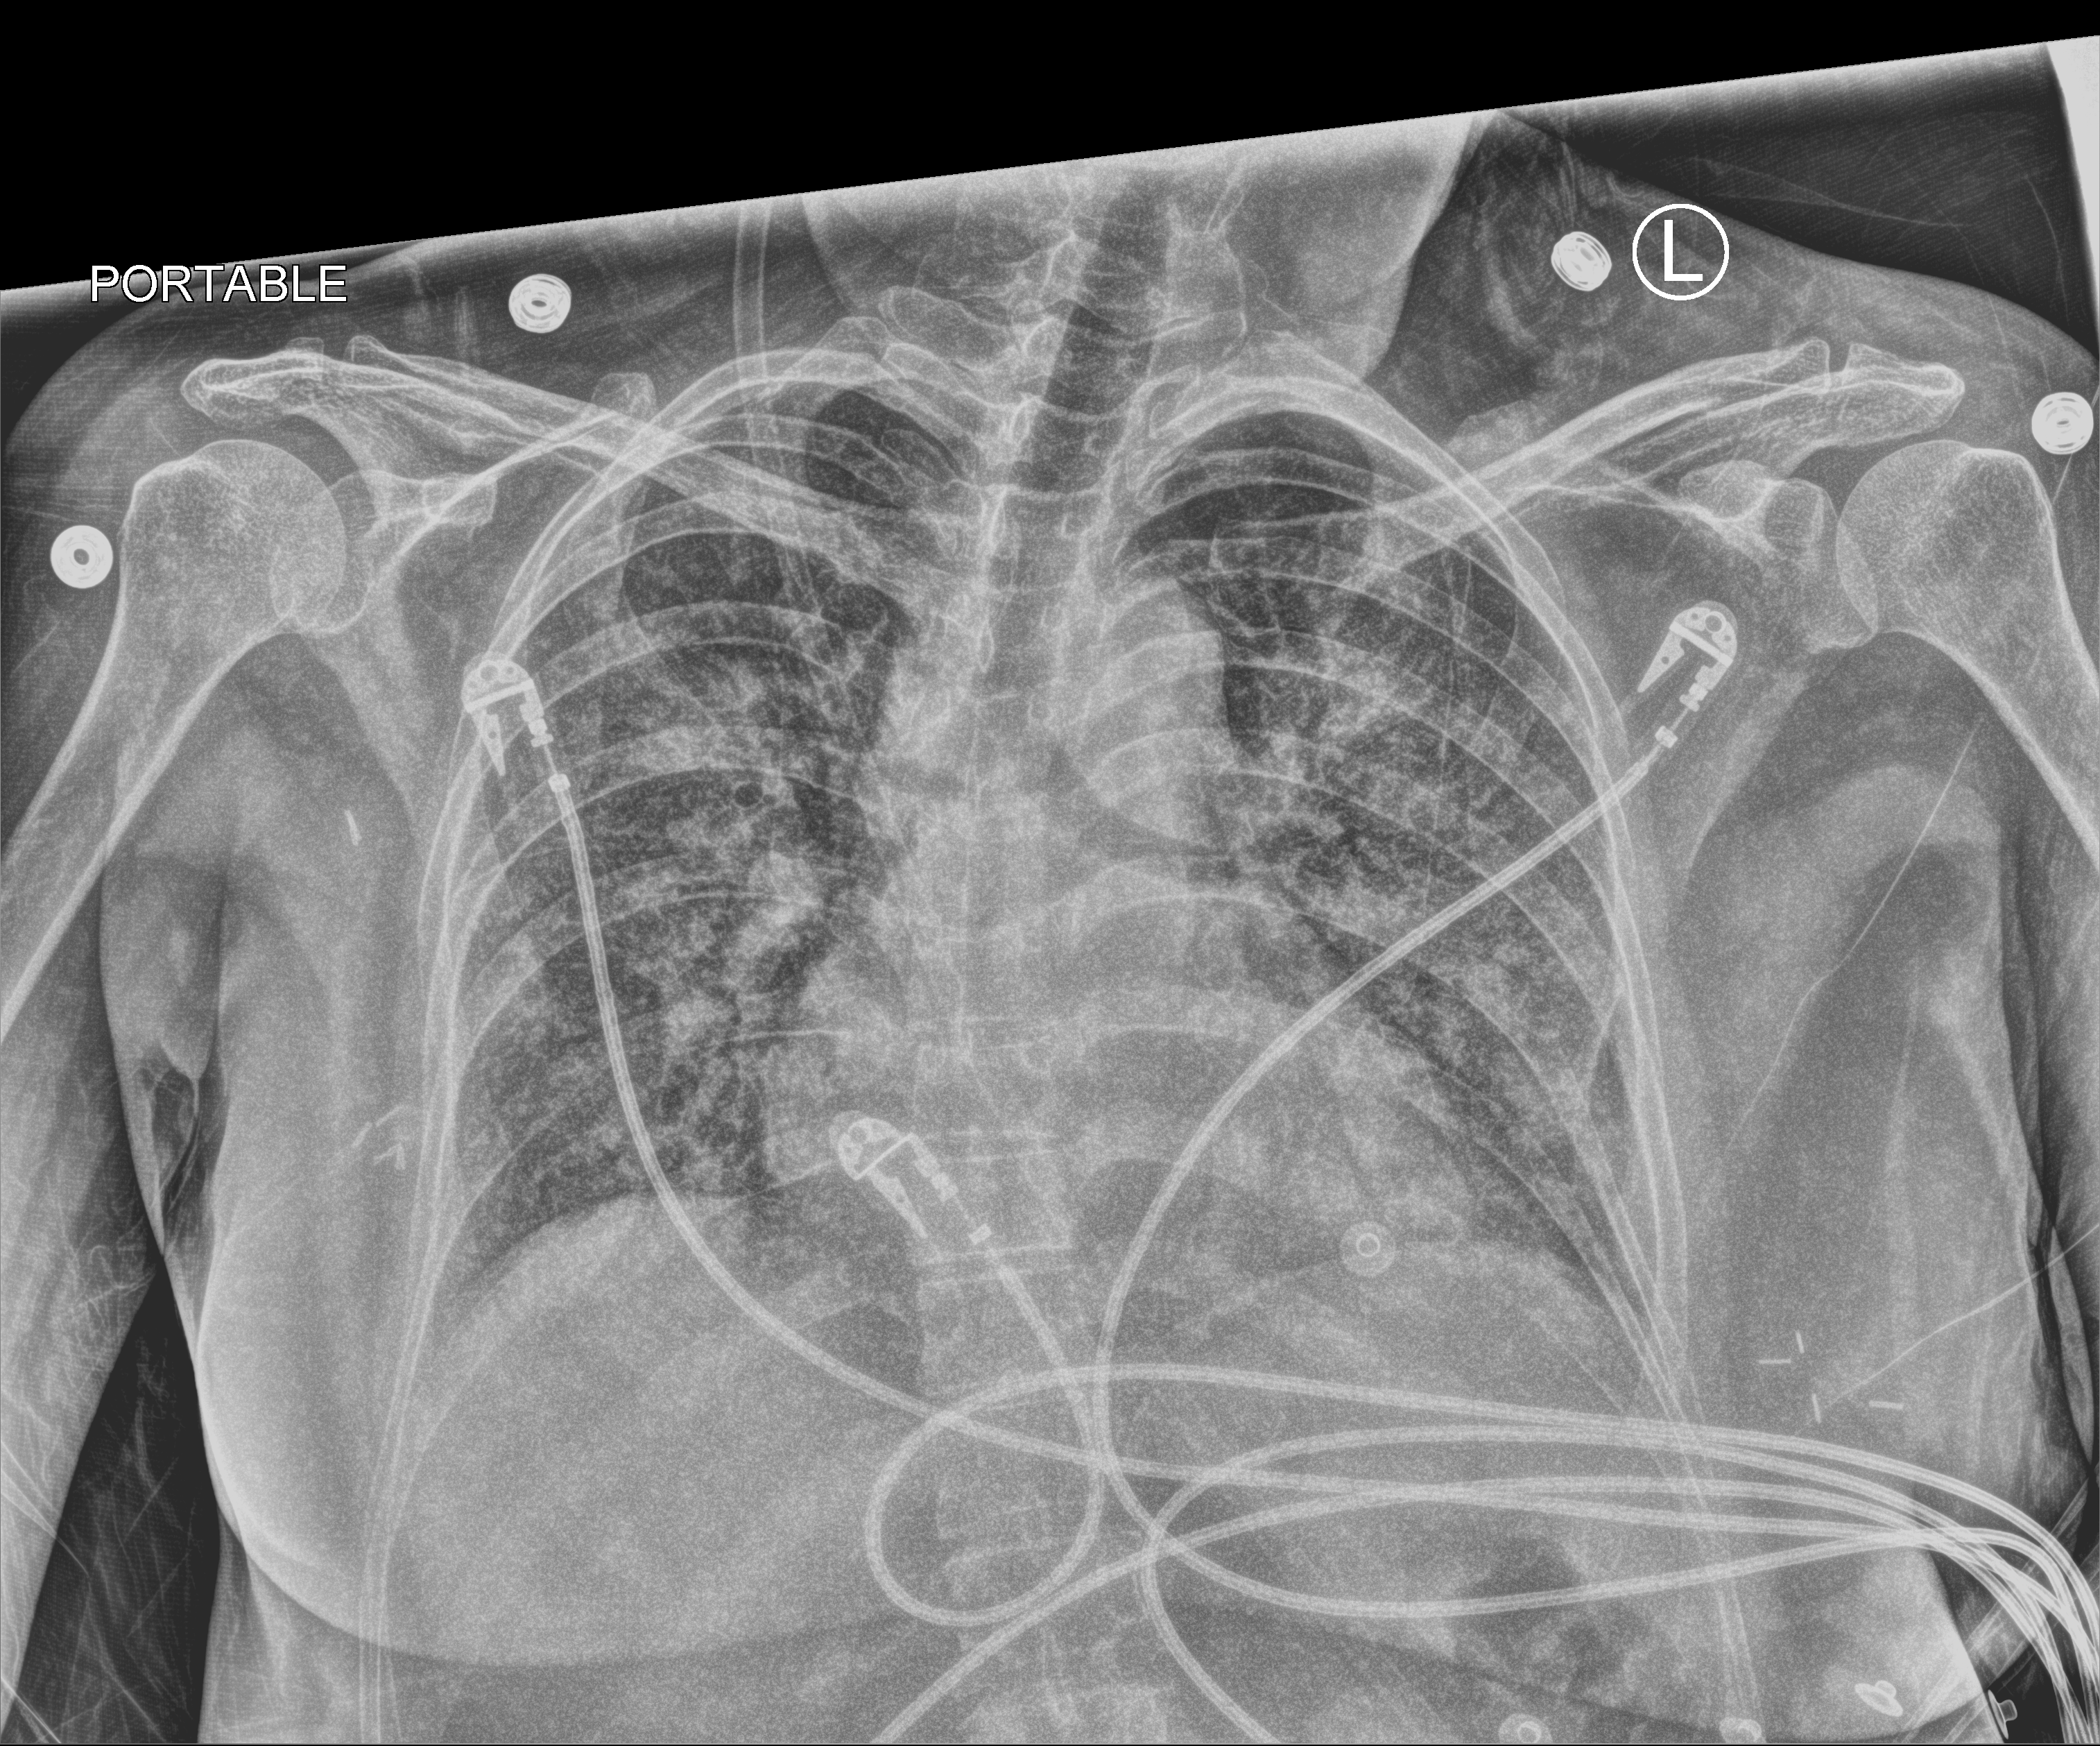
Portable chest radiograph, anteroposterior (AP) projection. Female patient hospitalised with COVID-19, age 18–59 years.
Hospital-stay facts (about this admission, not read from this image; timing relative to this image not recorded): mechanically ventilated during this hospital stay: yes; hypertension (admission record): no.